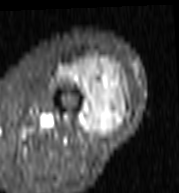
MRI of an extremity soft-tissue mass, one axial slice. Position 42 of 103 along the scan axis. STIR. MR volume resampled by the dataset authors to the PET/CT grid (not the native acquisition matrix). 3.27 mm slice thickness. 179 × 193 image matrix, field of view 175 × 188 mm. Female patient. Case-level facts recorded for this patient, not image findings: histological type: undifferentiated – high grade; grade: high; site of the primary tumour: left thigh.
Outlined on this slice (expert contour drawn on MRI and transferred to this co-registered scan by the dataset authors):
- gross tumour volume including surrounding oedema: bounding box [x1, y1, x2, y2] px = [57, 57, 128, 138]
- gross tumour volume (mass): [79, 59, 128, 138]